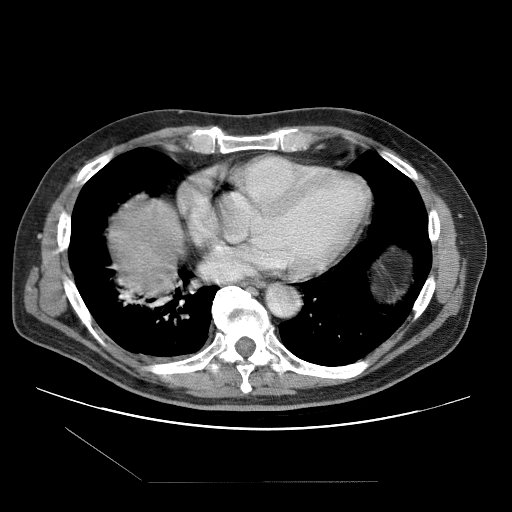
Contrast-enhanced abdominal CT (liver protocol), one axial slice; one of 2 acquisitions stored at this slice position; soft-tissue window (W 400 / L 40 HU); 2.5 mm slice thickness; 512 × 512 image matrix, field of view 400 × 400 mm. Case-level facts recorded for this patient, not image findings: diagnosis: hepatocellular carcinoma (patient treated with transarterial chemoembolisation; whether this scan precedes or follows treatment is not stated here); TNM stage (as recorded): Stage-IIIB.
Annotated regions visible in this slice (semi-automatic segmentation, software-assisted and operator-edited):
- liver parenchyma outside the tumour (the mass and vessels are separate outlines, so this box may not span the whole liver): bounding box [x1, y1, x2, y2] px = [108, 200, 184, 300]
- liver vessels: [124, 293, 130, 299]